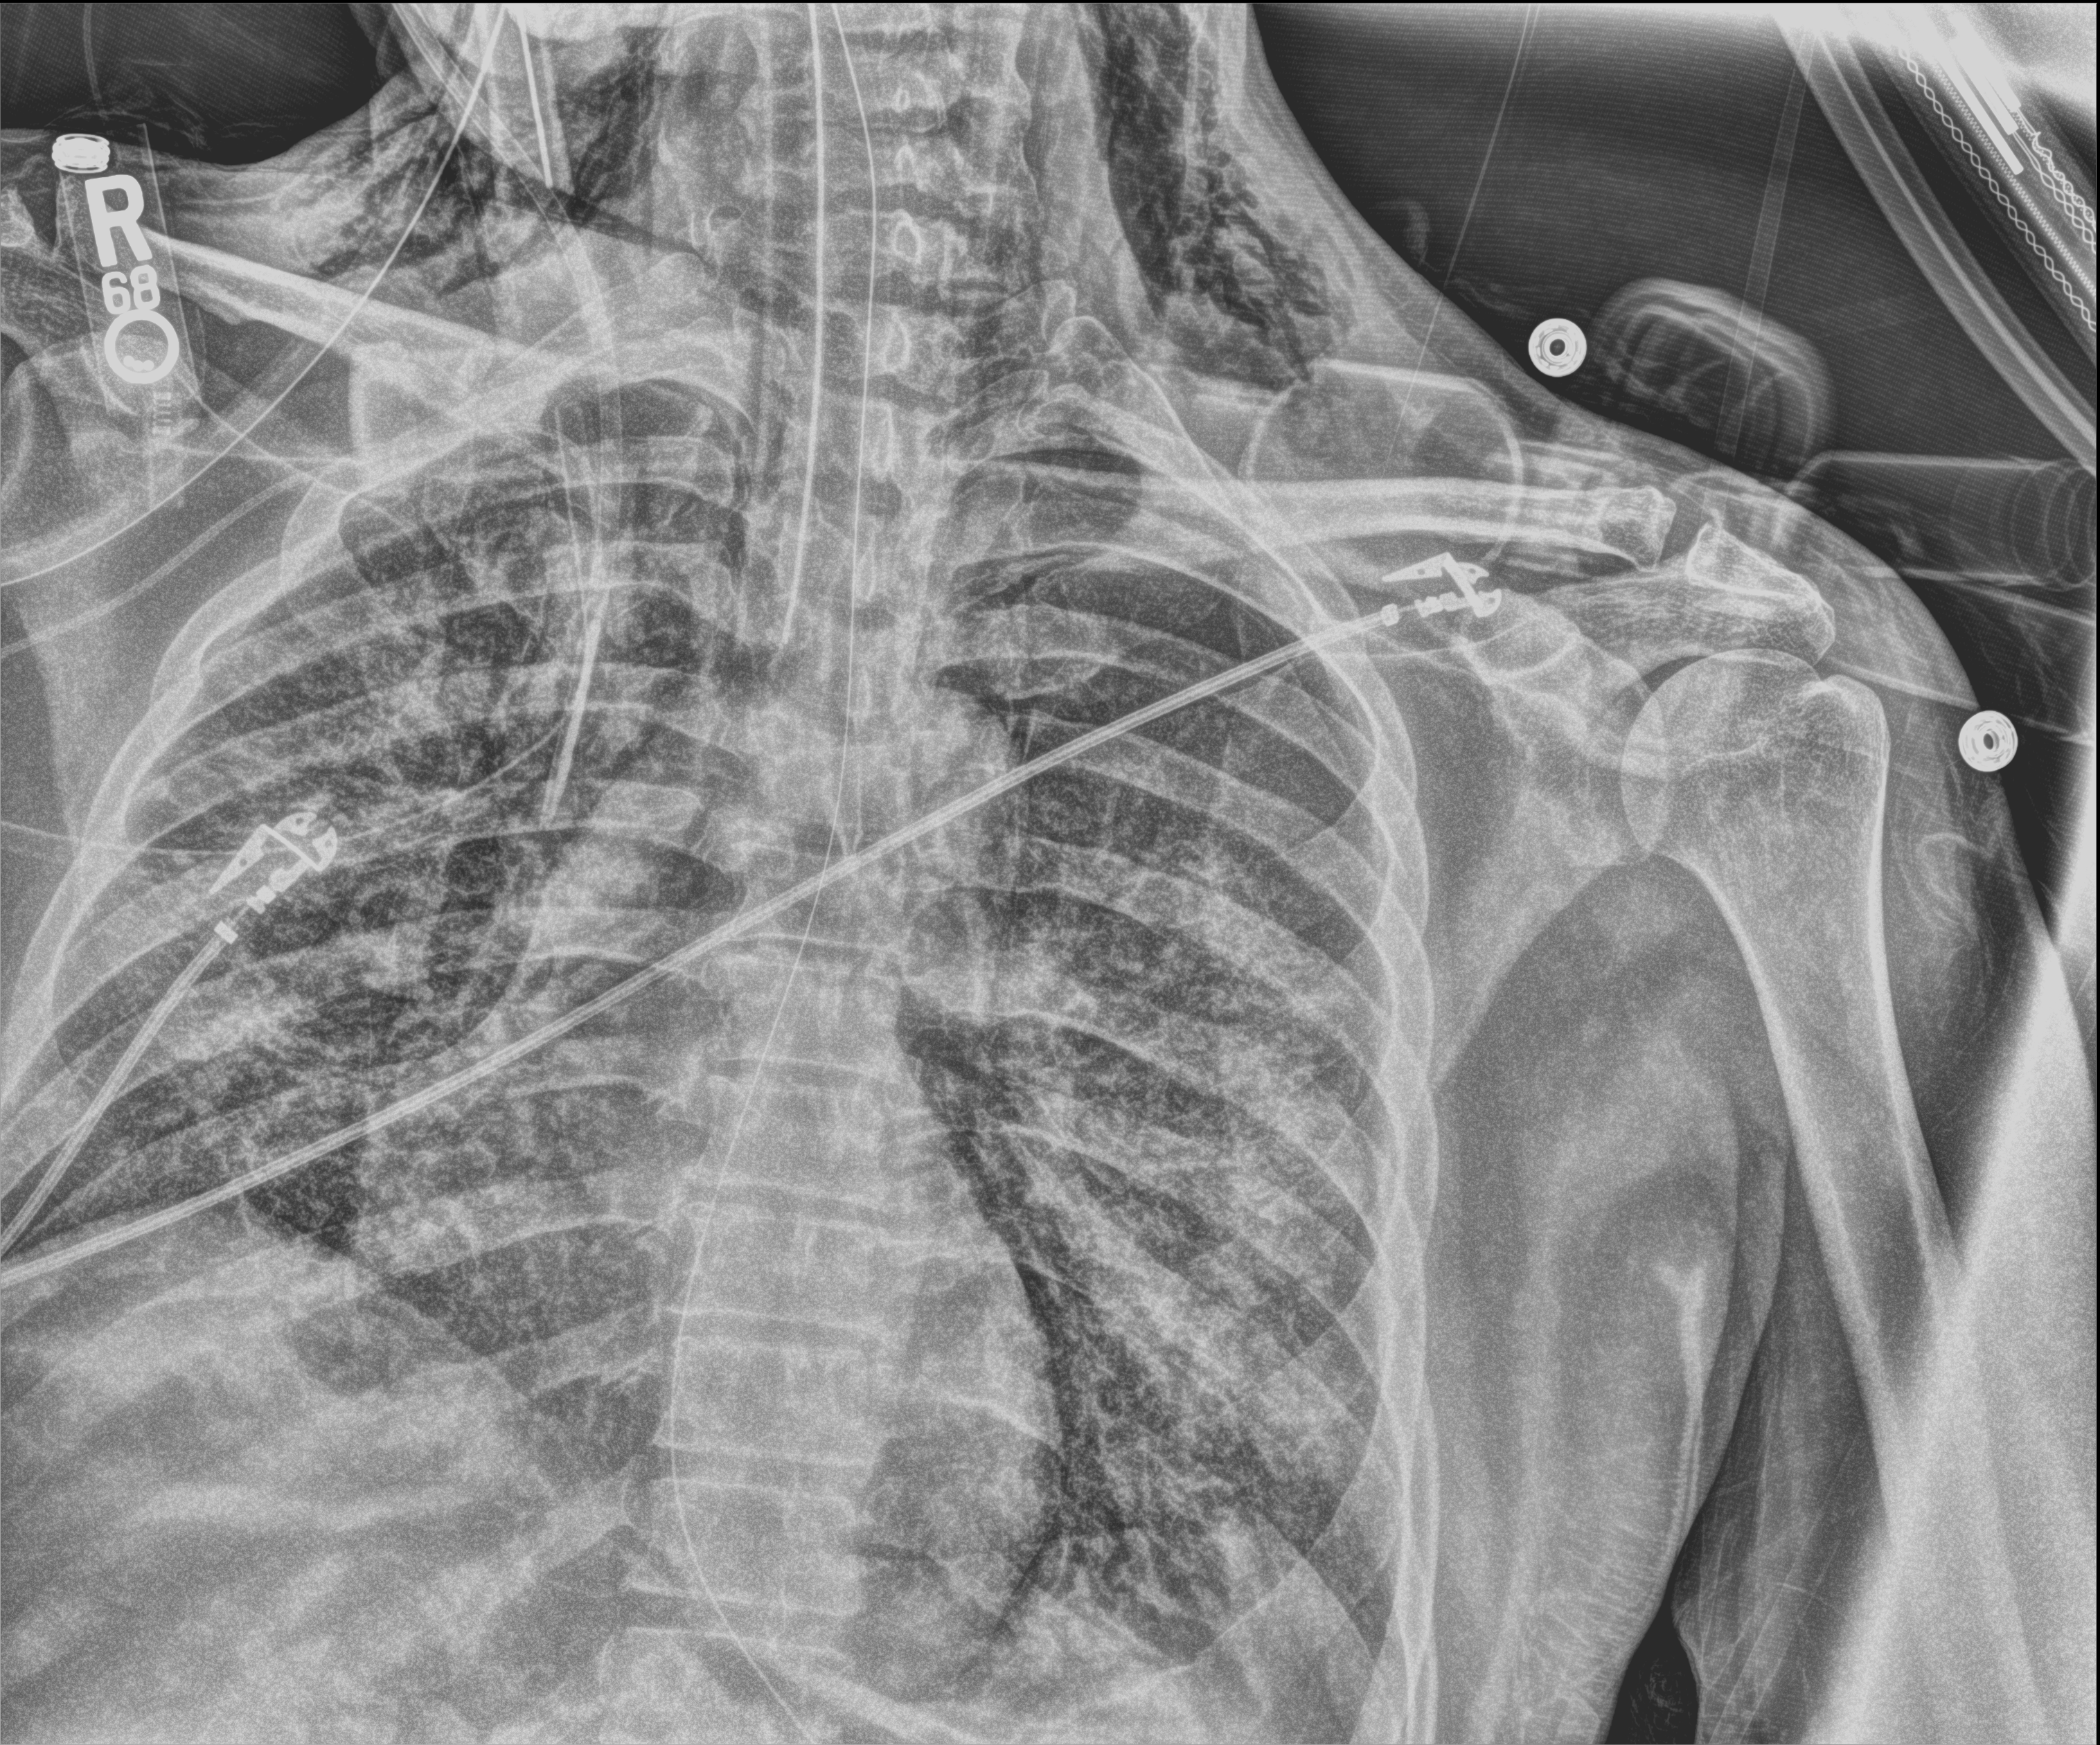
Chest X-ray (portable). Patient hospitalised with COVID-19; male, aged 18–59 years.
Hospital-stay facts (about this admission, not read from this image; timing relative to this image not recorded): admitted to intensive care during this hospital stay: yes; mechanically ventilated during this hospital stay: yes.